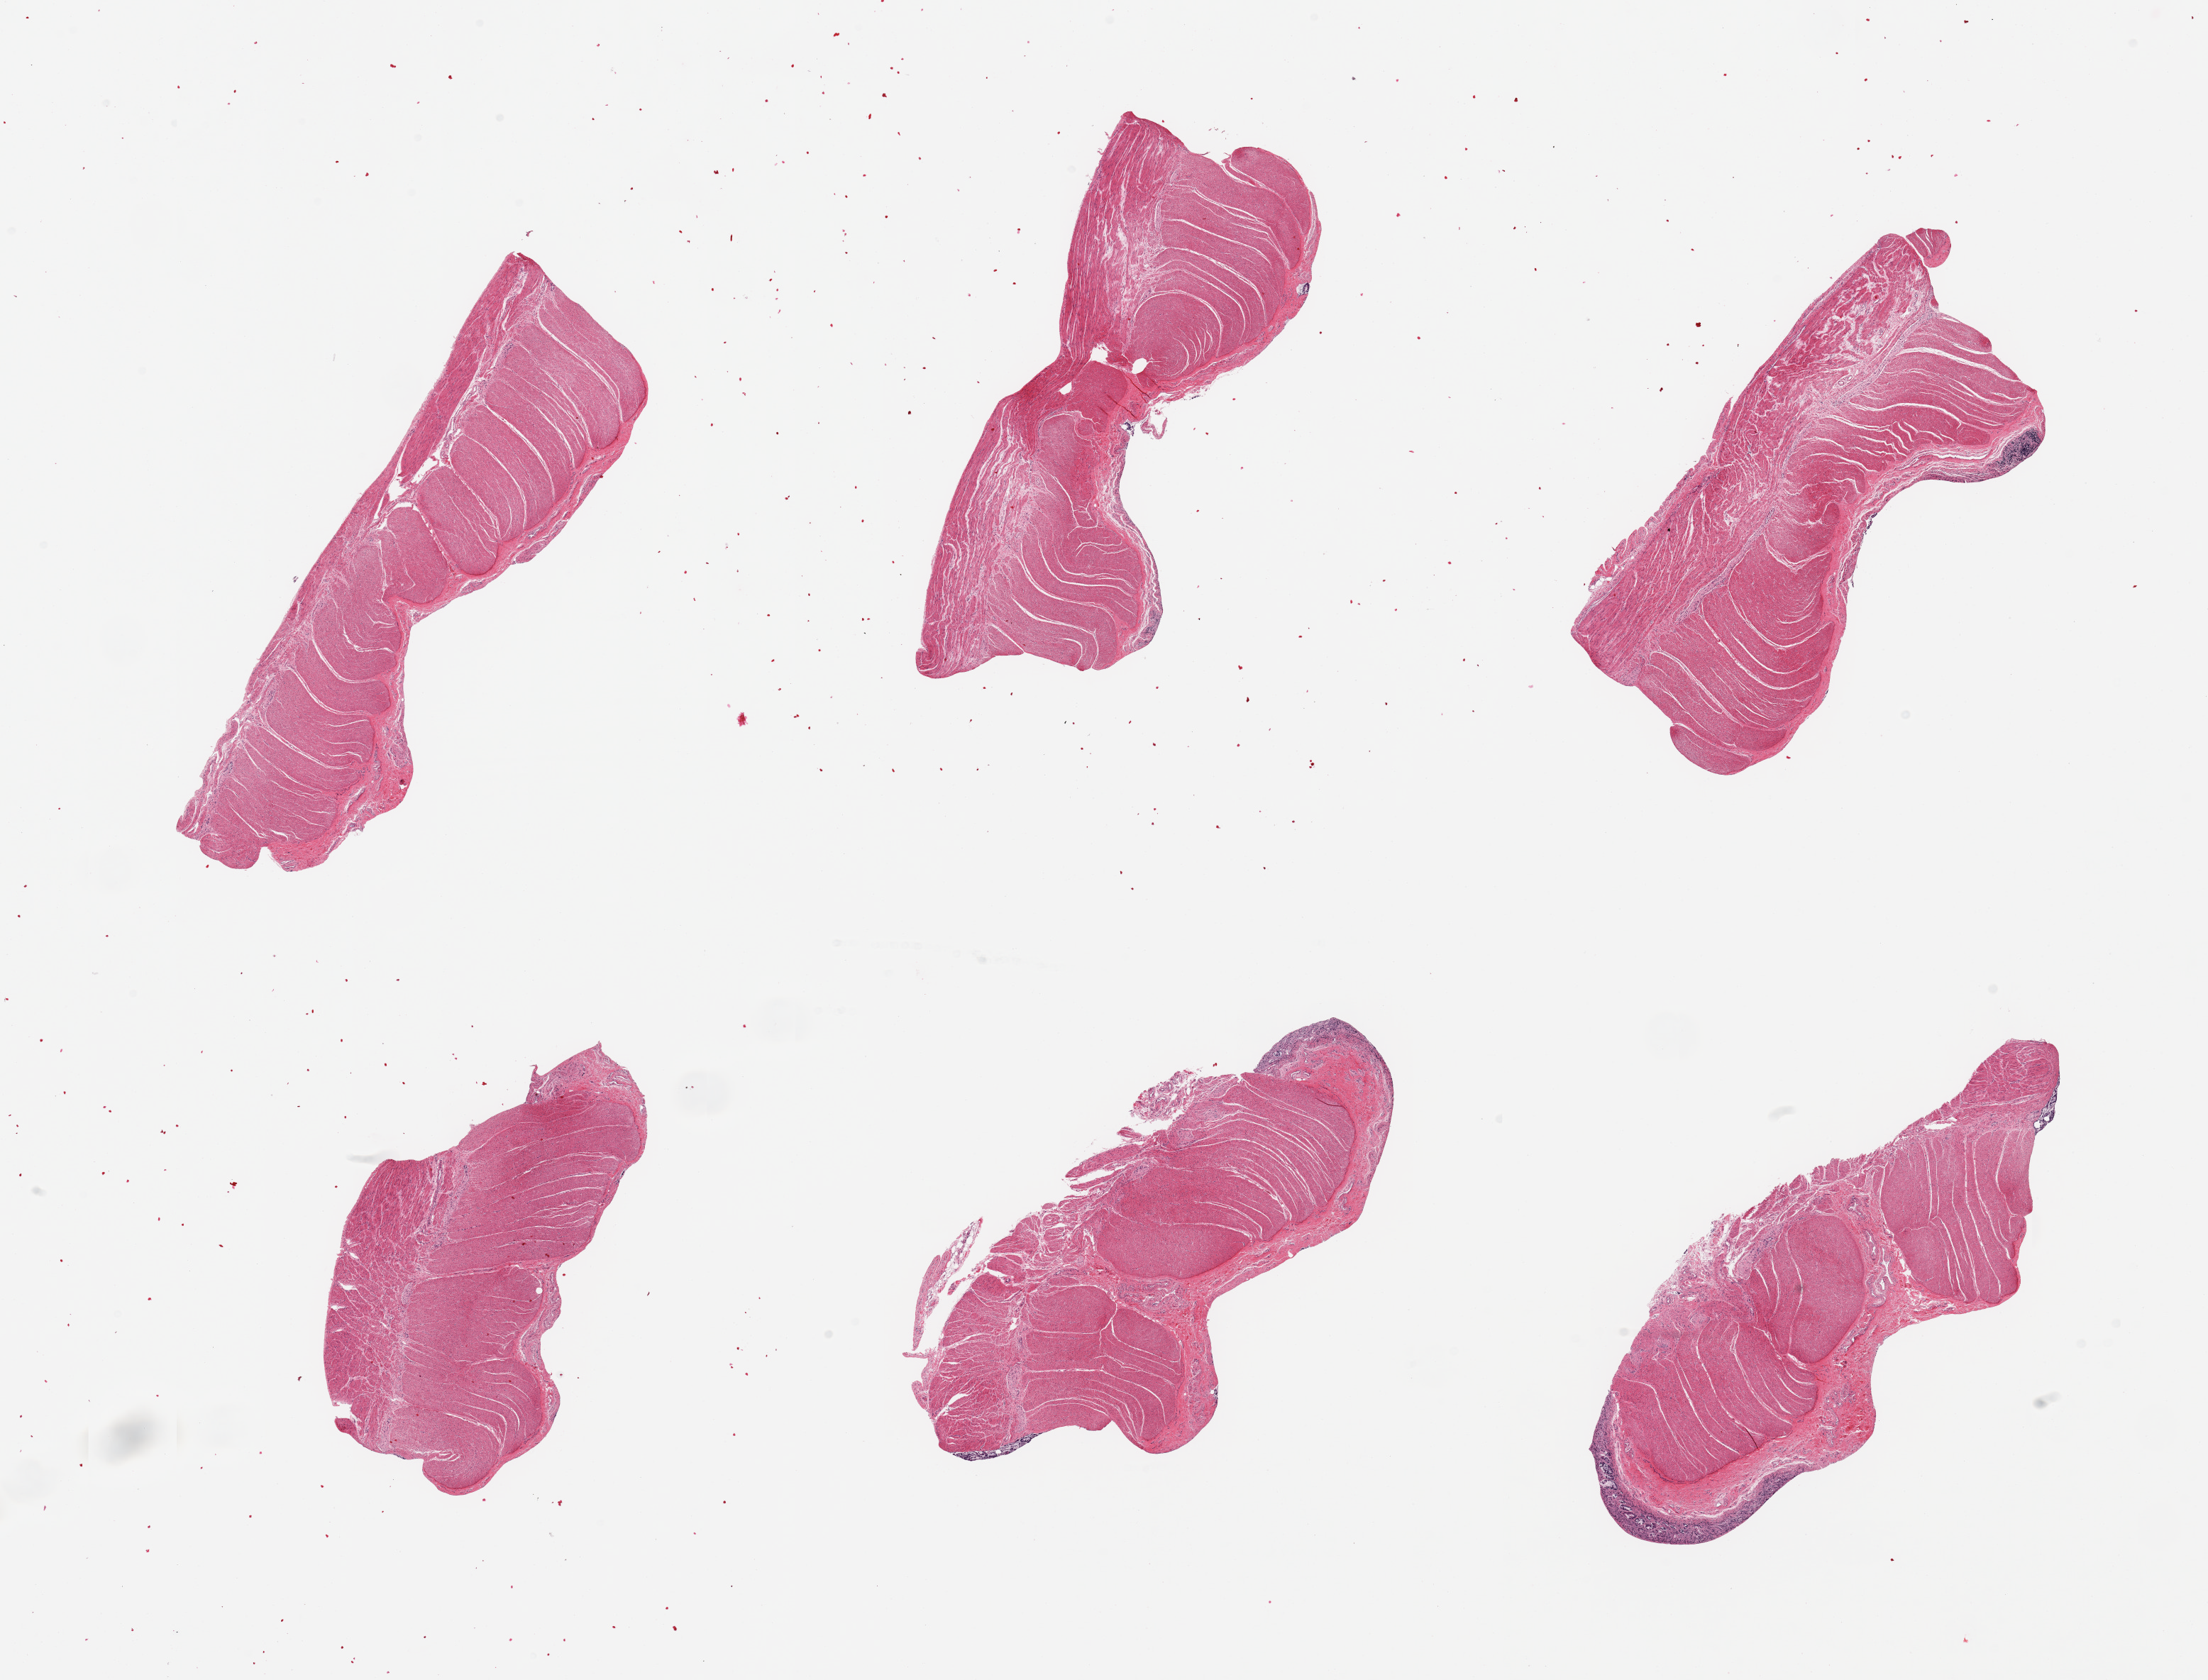
Digitized hematoxylin and eosin (H&E)-stained section, a low-resolution overview of the entire scanned area, about 24.6 x 18.7 mm (from a 20x scan), PAXgene-fixed, paraffin-embedded tissue, sampled site (target tissue): sigmoid colon, tissue donor sample. Female donor.
Reviewer comment on this tissue sample: 6 pieces, target muscularis, trace 'contaminant' mucosa.